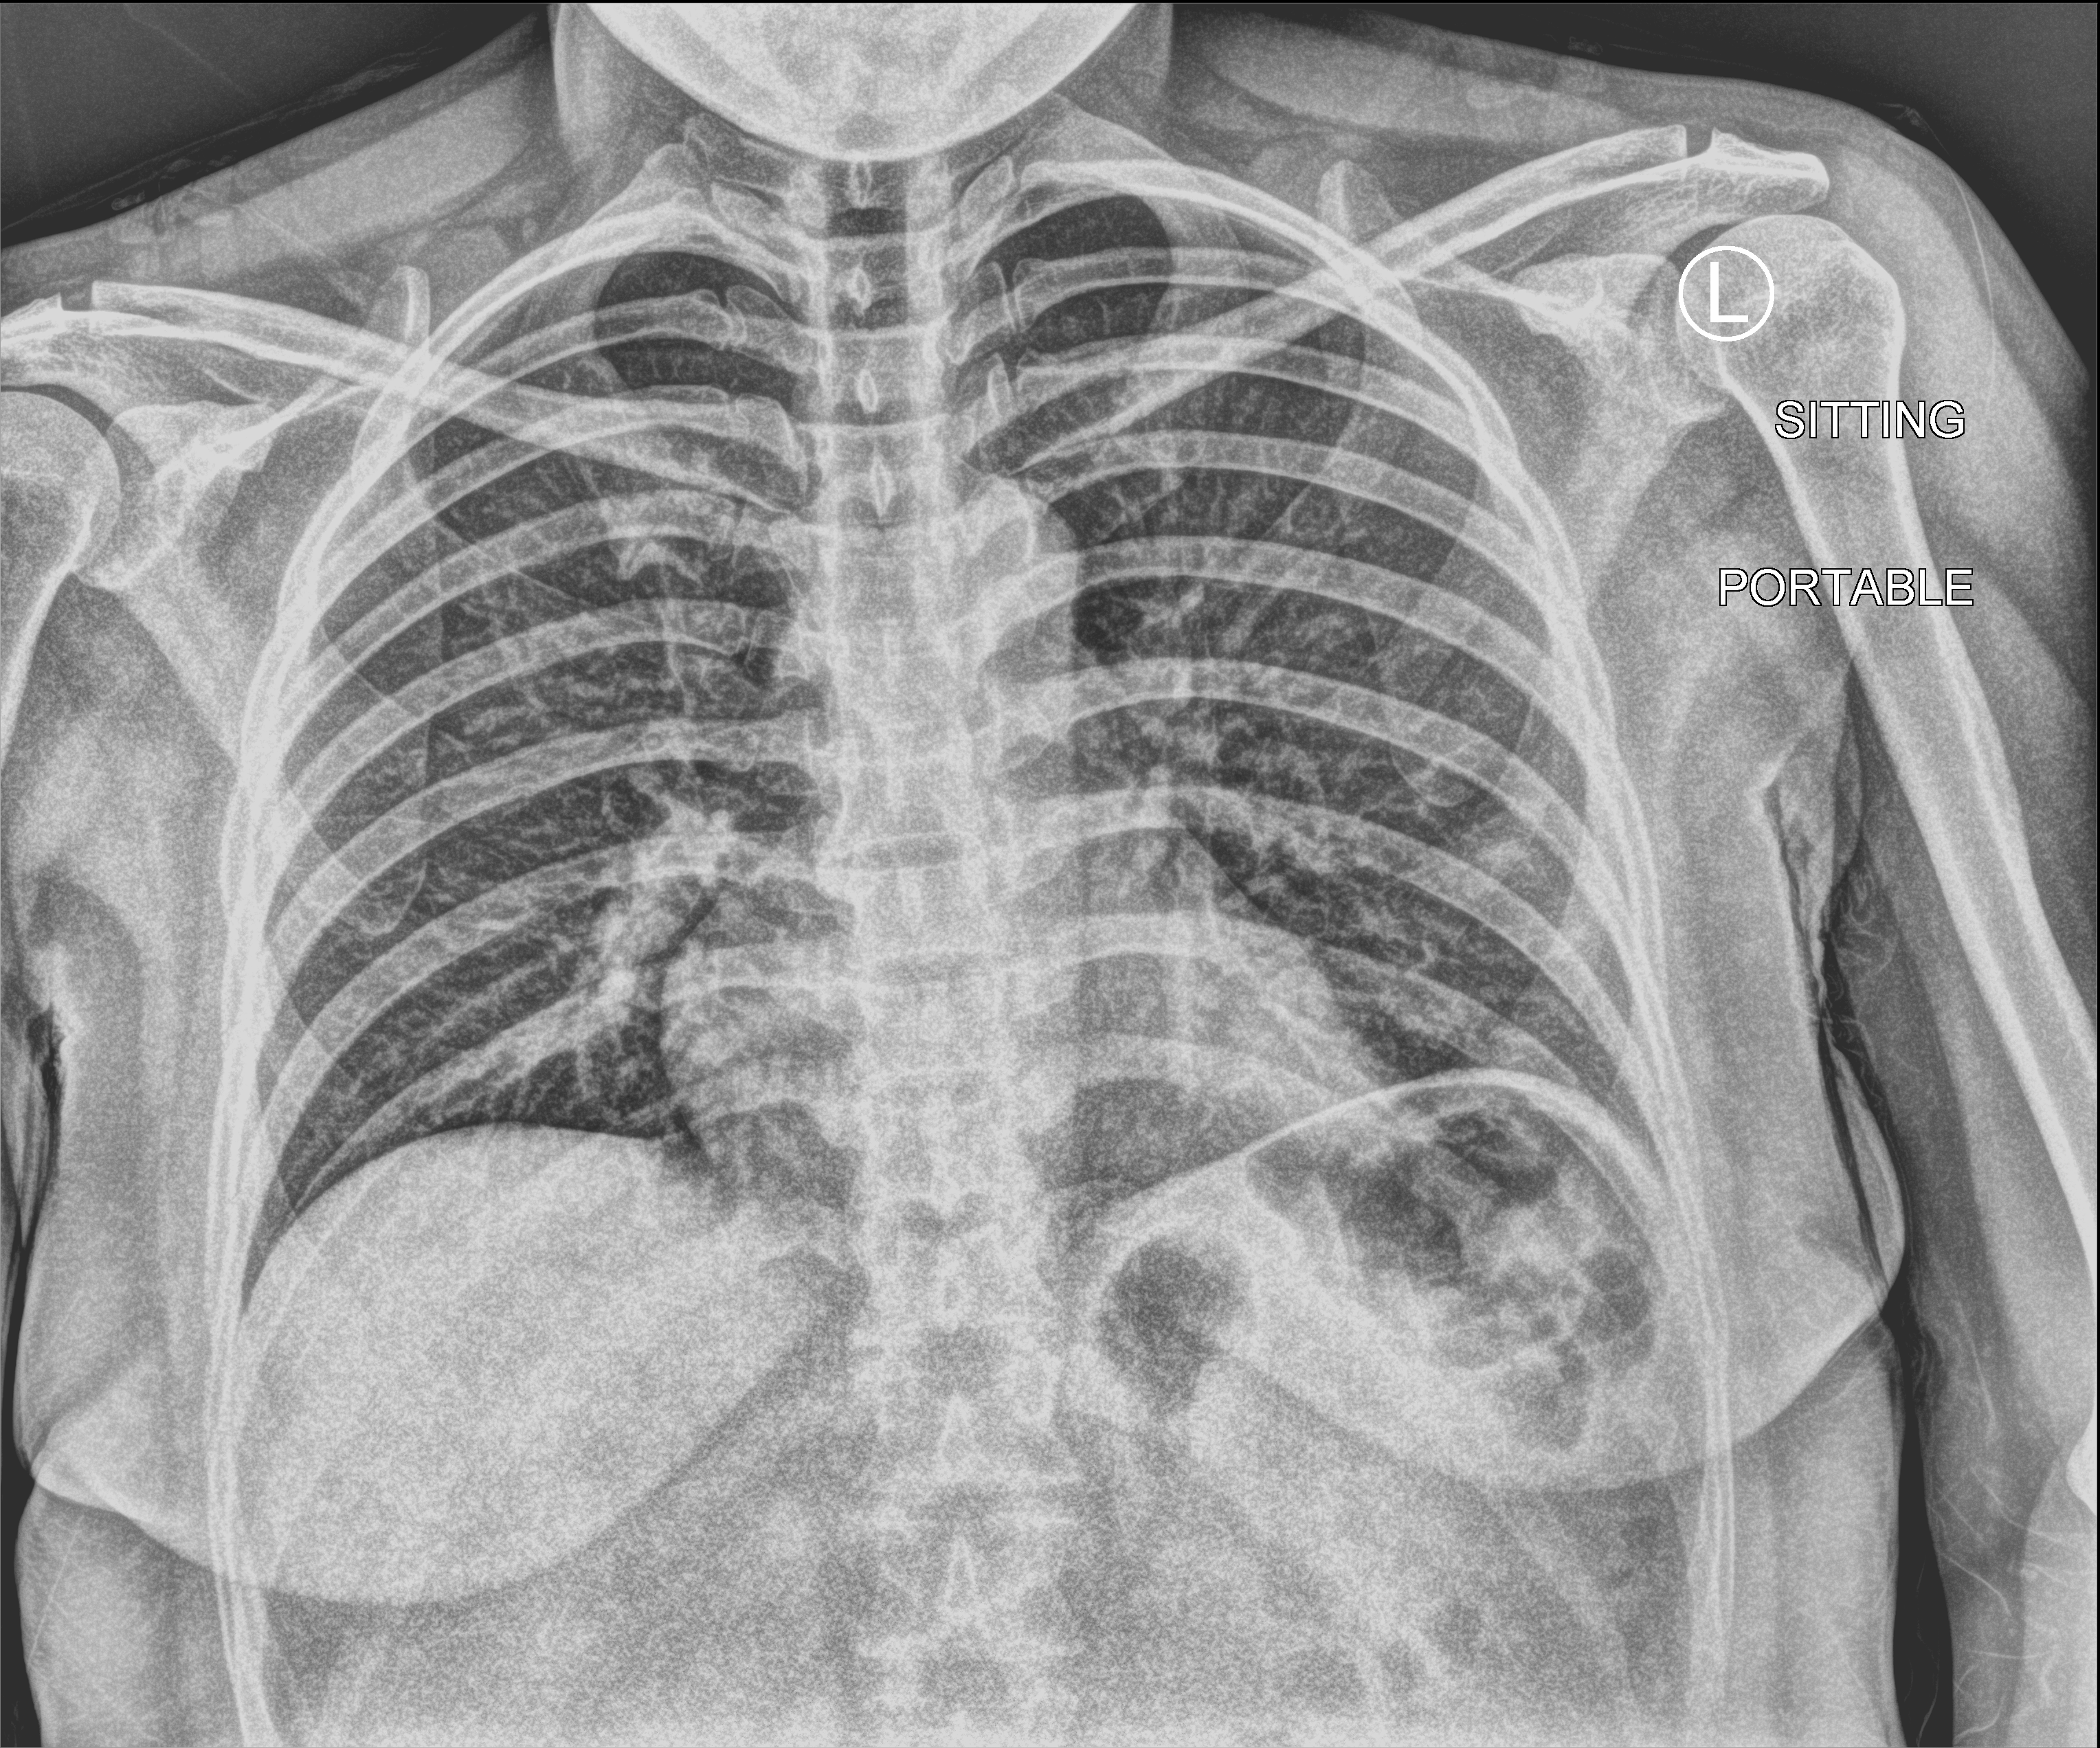
Chest X-ray (portable); anteroposterior (AP) projection. Female patient hospitalised with COVID-19, age 18–59 years.
Admission-level facts for this patient (not findings on this image; timing relative to this image not recorded):
- length of hospital stay: 1 day